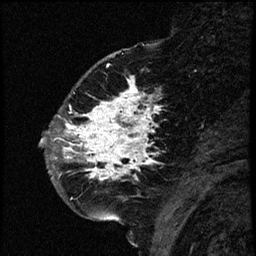
Breast MRI (dynamic contrast-enhanced), one sagittal slice; slice 21 of 66 in the series (ordered by position); dynamic contrast-enhanced study with each time point stored as its own series, time point 2 of 3 at this slice position (early post-contrast, ordered by acquisition time); 1.5 T; TE 4.2 ms, TR 17.6 ms; 2 mm slice thickness; 256 × 256 image matrix, field of view 200 × 200 mm. Female patient. From the clinical record (not read from this slice): setting: breast cancer imaged before/during neoadjuvant chemotherapy; receptor status: HER2-positive.
Structures marked on this image (semi-automatic segmentation, software-assisted and operator-edited):
- analysis volume of interest (the breast-tissue region the enhancement analysis was run in; not a lesion): bounding box <52,69,177,209> (left, top, right, bottom; pixels)
- tumour enhancement mask (voxels above the 100 % enhancement threshold inside the analysis volume of interest): <52,79,160,181>